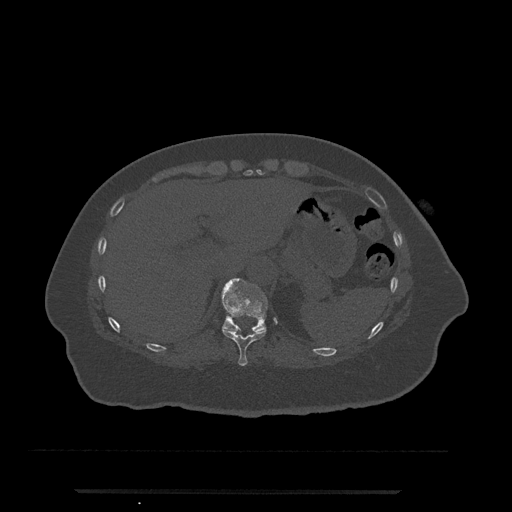
CT including the spine, one axial slice; position 260 of 797 along the scan axis; bone window (W 1800 / L 400 HU); 512 × 512 image matrix. Patient: female, 51 years. Case-level facts recorded for this patient, not image findings: primary cancer: neuro; vertebrae with lytic lesions (as recorded): T8.
Outlined on this slice (semi-automatically segmented with operator editing):
- T10 vertebra: bounding box [x1, y1, x2, y2] px = [222, 327, 267, 366]
- T11 vertebra: [222, 278, 268, 333]